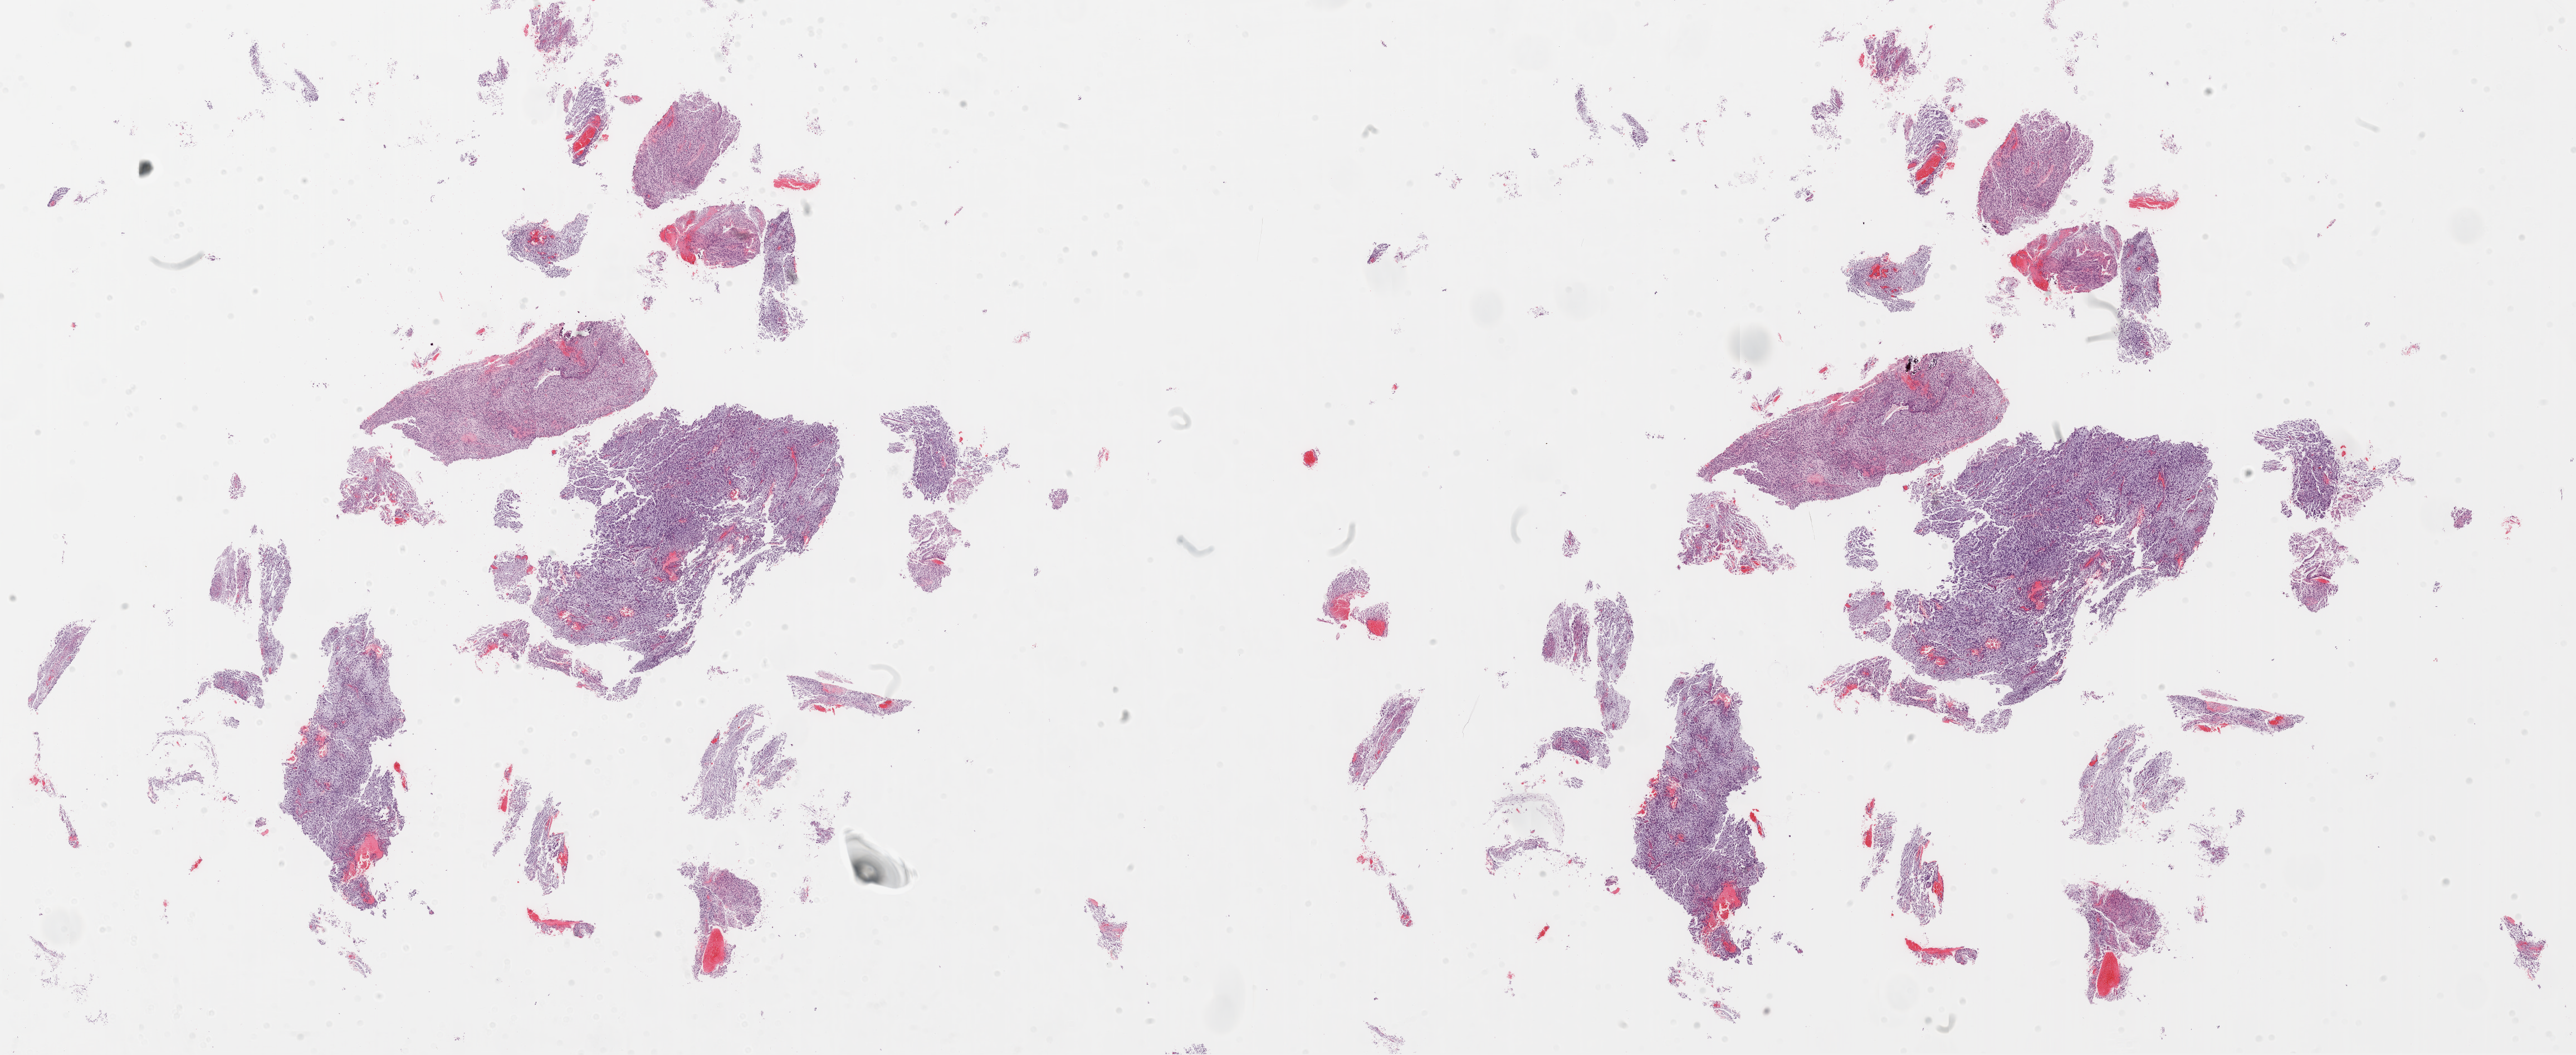
Whole-slide histology image, H&E-stained, whole scanned area (about 37.1 x 15.2 mm, acquisition: 20x scan) shown as a low-resolution overview, formalin-fixed paraffin-embedded (FFPE) diagnostic section, brain, primary tumour sample. Patient: female, age at initial diagnosis 17 years.
Histologic diagnosis: Glioblastoma.